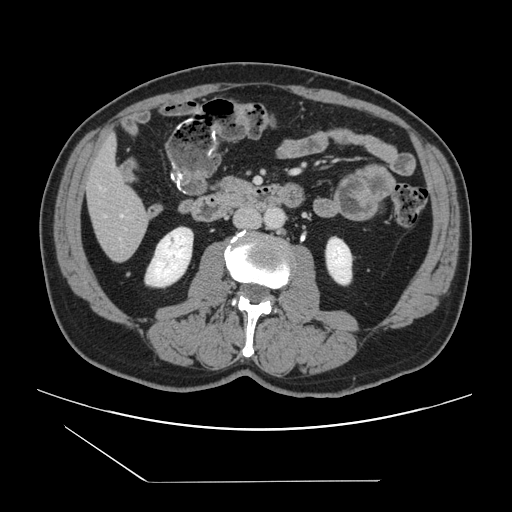
Contrast-enhanced abdominal CT, one axial slice. Position 34 of 157 along the scan axis. 120 kVp. Intravenous contrast given. Soft-tissue window (W 400 / L 40 HU). 2.5 mm slice thickness. 512 × 512 image matrix, field of view 407 × 407 mm. Male patient, age 61 years. Case-level facts recorded for this patient, not image findings: diagnosis: colorectal cancer liver metastases, imaged before liver resection.
Outlined on this slice (manually delineated by an expert):
- hepatic veins: box from (x=121, y=214) to (x=123, y=217) px
- liver: (x=86, y=141)–(x=150, y=261)
- planned liver remnant (the part of the liver to remain after resection): (x=86, y=140)–(x=145, y=219)